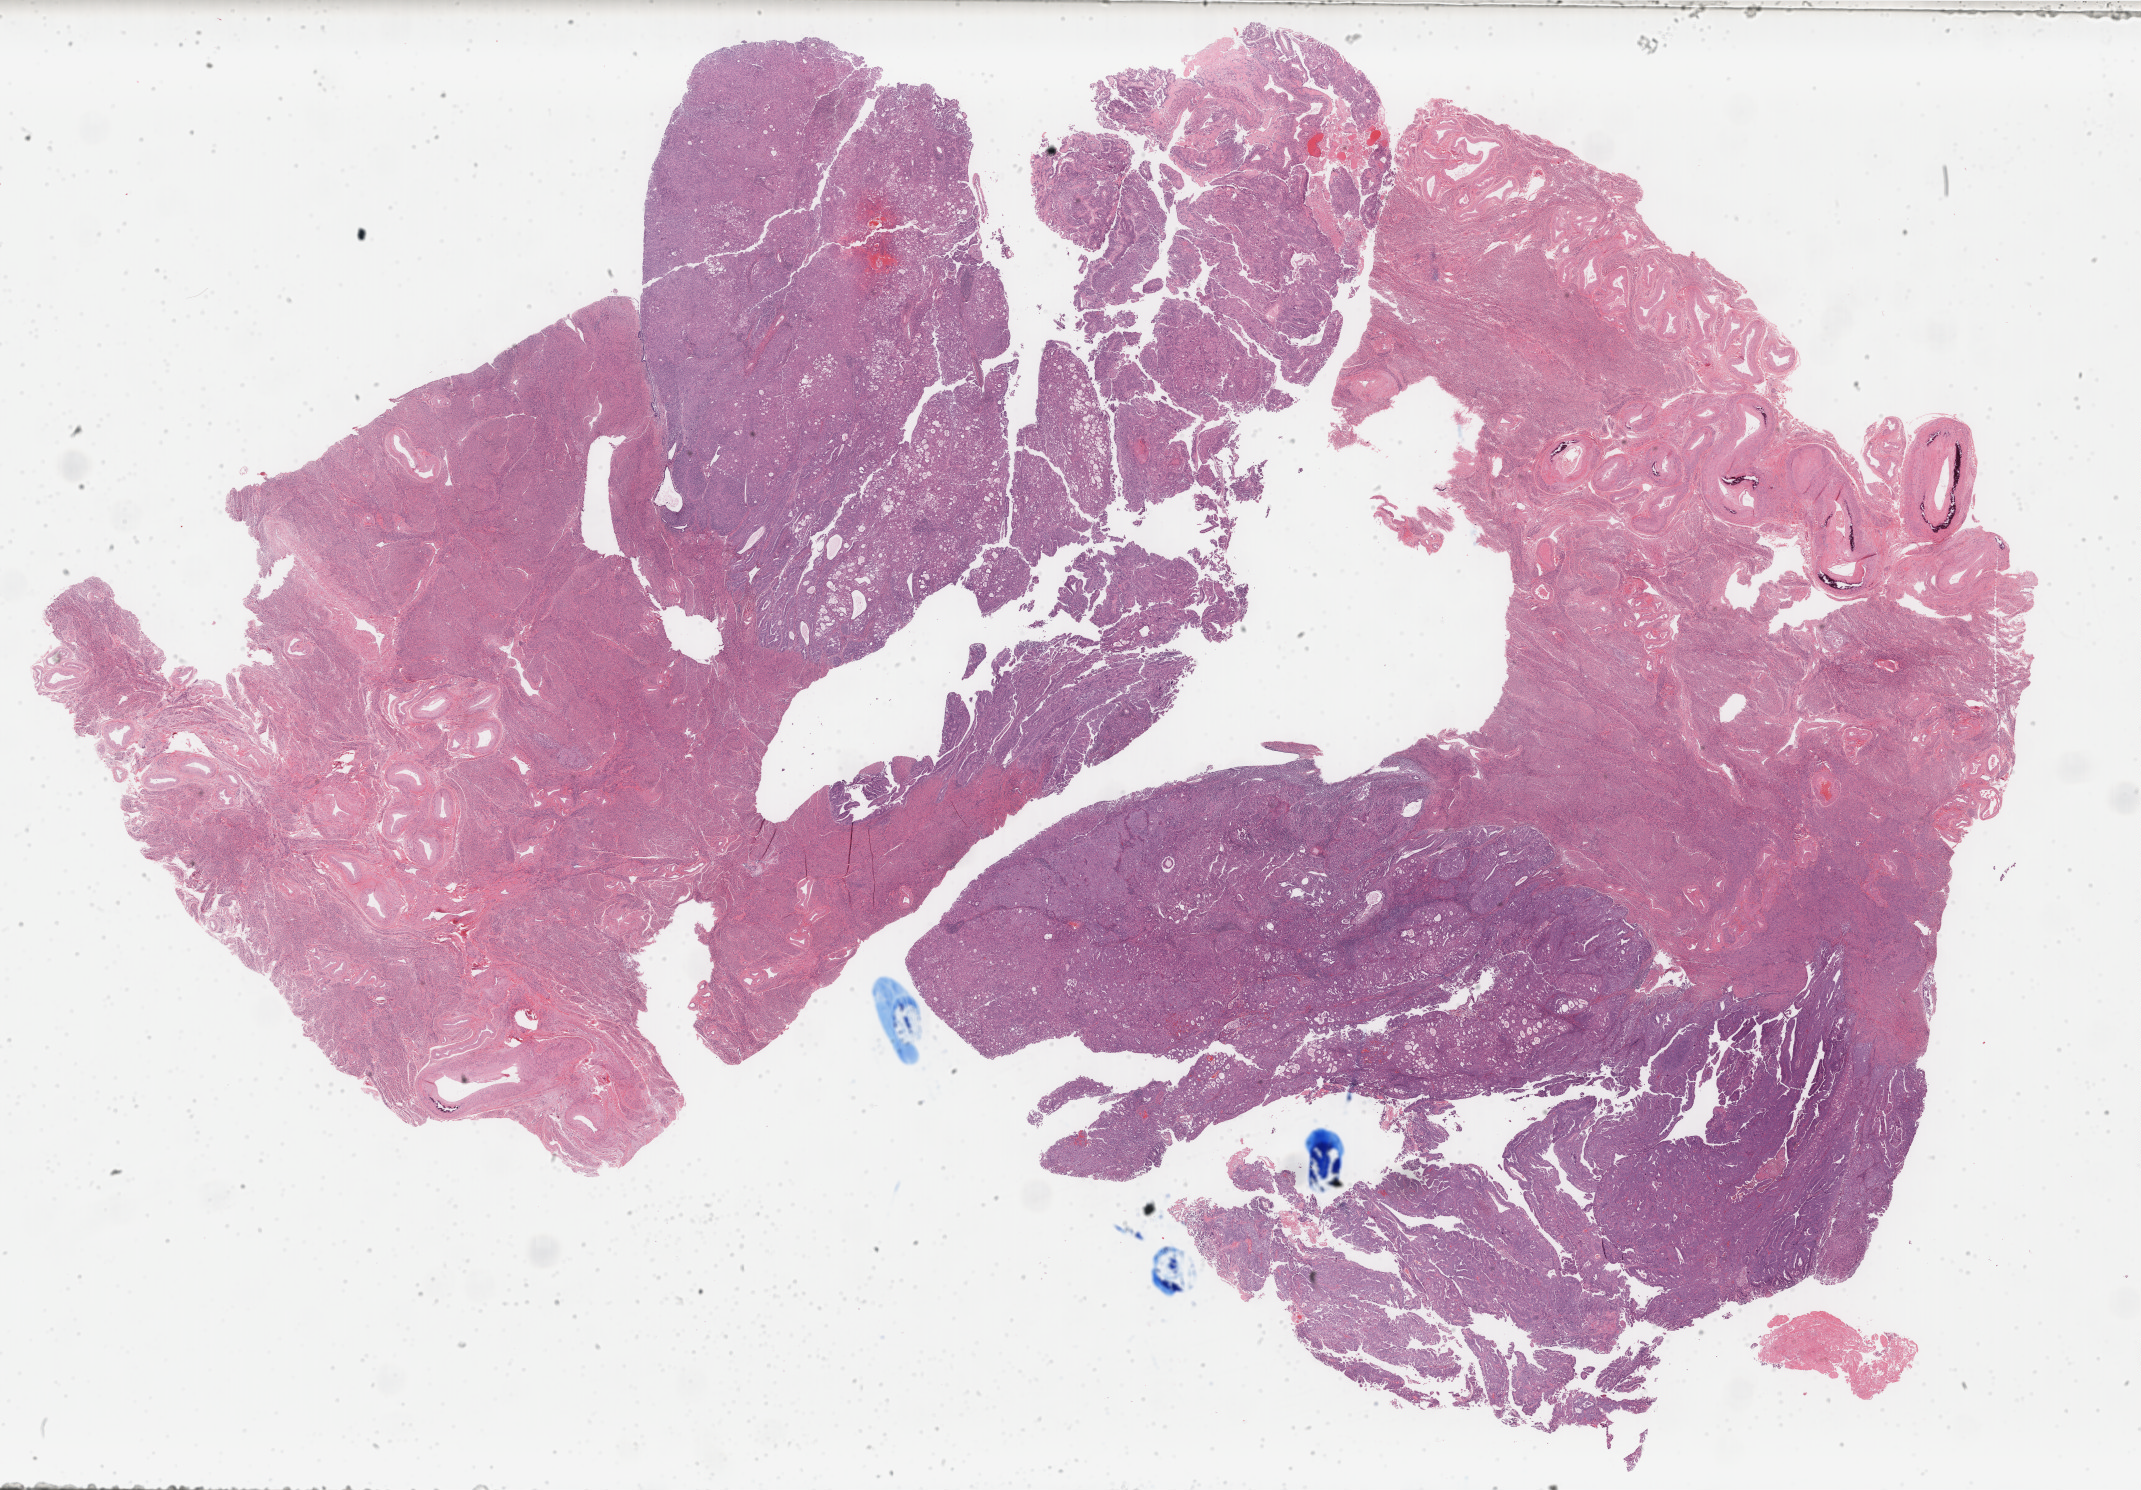
H&E whole-slide image, shown as a low-resolution overview of the whole scanned area (about 34.0 x 23.7 mm). FFPE section. Sample: primary tumour, uterus. Female, age 77 years at initial diagnosis. Histologic grade: G3 (poorly differentiated).
FIGO stage: IA. Diagnosis: Endometrioid adenocarcinoma, NOS (endometrium).